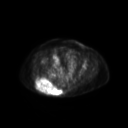
FDG PET of an extremity soft-tissue mass (from a PET/CT study), one axial slice. Slice 65 of 267 in the series (ordered by position). 3.27 mm slice thickness. 128 × 128 image matrix, field of view 600 × 600 mm. Female patient, age 60 years. Case-level facts recorded for this patient, not image findings: histological type: spindle cell suggestive of myxofibrosarcoma; grade: intermediate; site of the primary tumour: right buttock.
Outlined on this slice (expert contour drawn on MRI and transferred to this co-registered scan by the dataset authors):
- gross tumour volume (mass): bounding box [x1, y1, x2, y2] px = [36, 78, 63, 96]